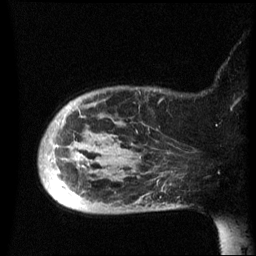
Breast MRI (dynamic contrast-enhanced), one sagittal slice; slice 11 of 60 in the series (ordered by position); dynamic contrast-enhanced series, image 2 of 3 at this slice position (ordered by acquisition); 1.5 T; TE 4.2 ms, TR 8.4 ms; 256 × 256 image matrix, field of view 220 × 220 mm. Patient: female, 49 years.
Structures marked on this image (semi-automatic segmentation, software-assisted and operator-edited):
- analysis volume of interest (the breast-tissue region the enhancement analysis was run in; not a lesion): bounding box <39,86,184,215> (left, top, right, bottom; pixels)
- tumour enhancement mask (voxels above the 70 % enhancement threshold inside the analysis volume of interest): <67,104,97,189>